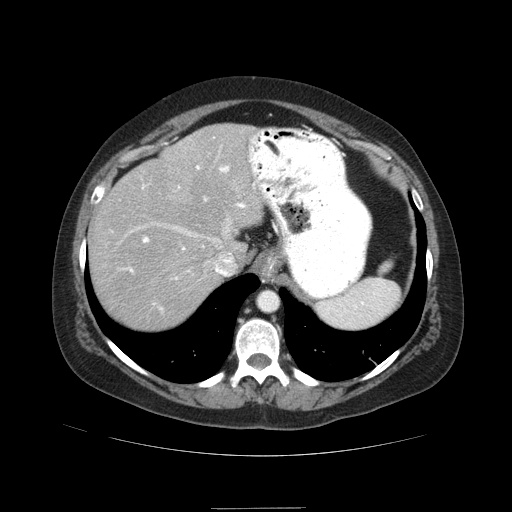
Contrast-enhanced abdominal CT (liver protocol), one axial slice. Slice 68 of 89 in the series (ordered by position). Reconstruction kernel STANDARD. 120 kVp. Soft-tissue window (W 400 / L 40 HU). 2.5 mm slice thickness. 512 × 512 image matrix, field of view 400 × 400 mm. From the clinical record (not read from this slice): diagnosis: hepatocellular carcinoma (patient treated with transarterial chemoembolisation; whether this scan precedes or follows treatment is not stated here); TNM stage (as recorded): Stage-IIIB; Child-Pugh class: A.
Outlined on this slice (semi-automatically segmented with operator editing):
- abdominal aorta: box from (x=259, y=292) to (x=278, y=311) px
- liver parenchyma outside the tumour (the mass and vessels are separate outlines, so this box may not span the whole liver): (x=88, y=124)–(x=266, y=328)
- liver vessels: (x=126, y=136)–(x=265, y=310)